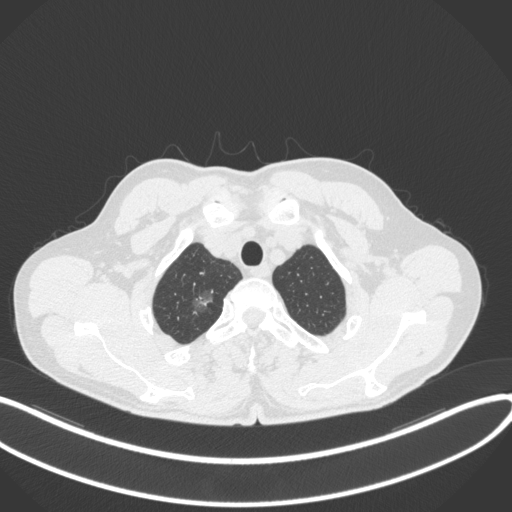
Chest CT, one axial slice; slice 341 of 407 in the series (ordered by position); reconstruction kernel B31f; 120 kVp; lung window (W 1500 / L -600 HU); 1 mm slice thickness; 512 × 512 image matrix. Male patient, age 58 years. Case-level facts recorded for this patient, not image findings: clinical TNM (as recorded): T1c N0 M0; histopathological grade: G1-2.
Outlined on this slice (bounding box drawn by a radiologist):
- lung tumour (recorded histology: adenocarcinoma): box from (x=186, y=285) to (x=223, y=314) px